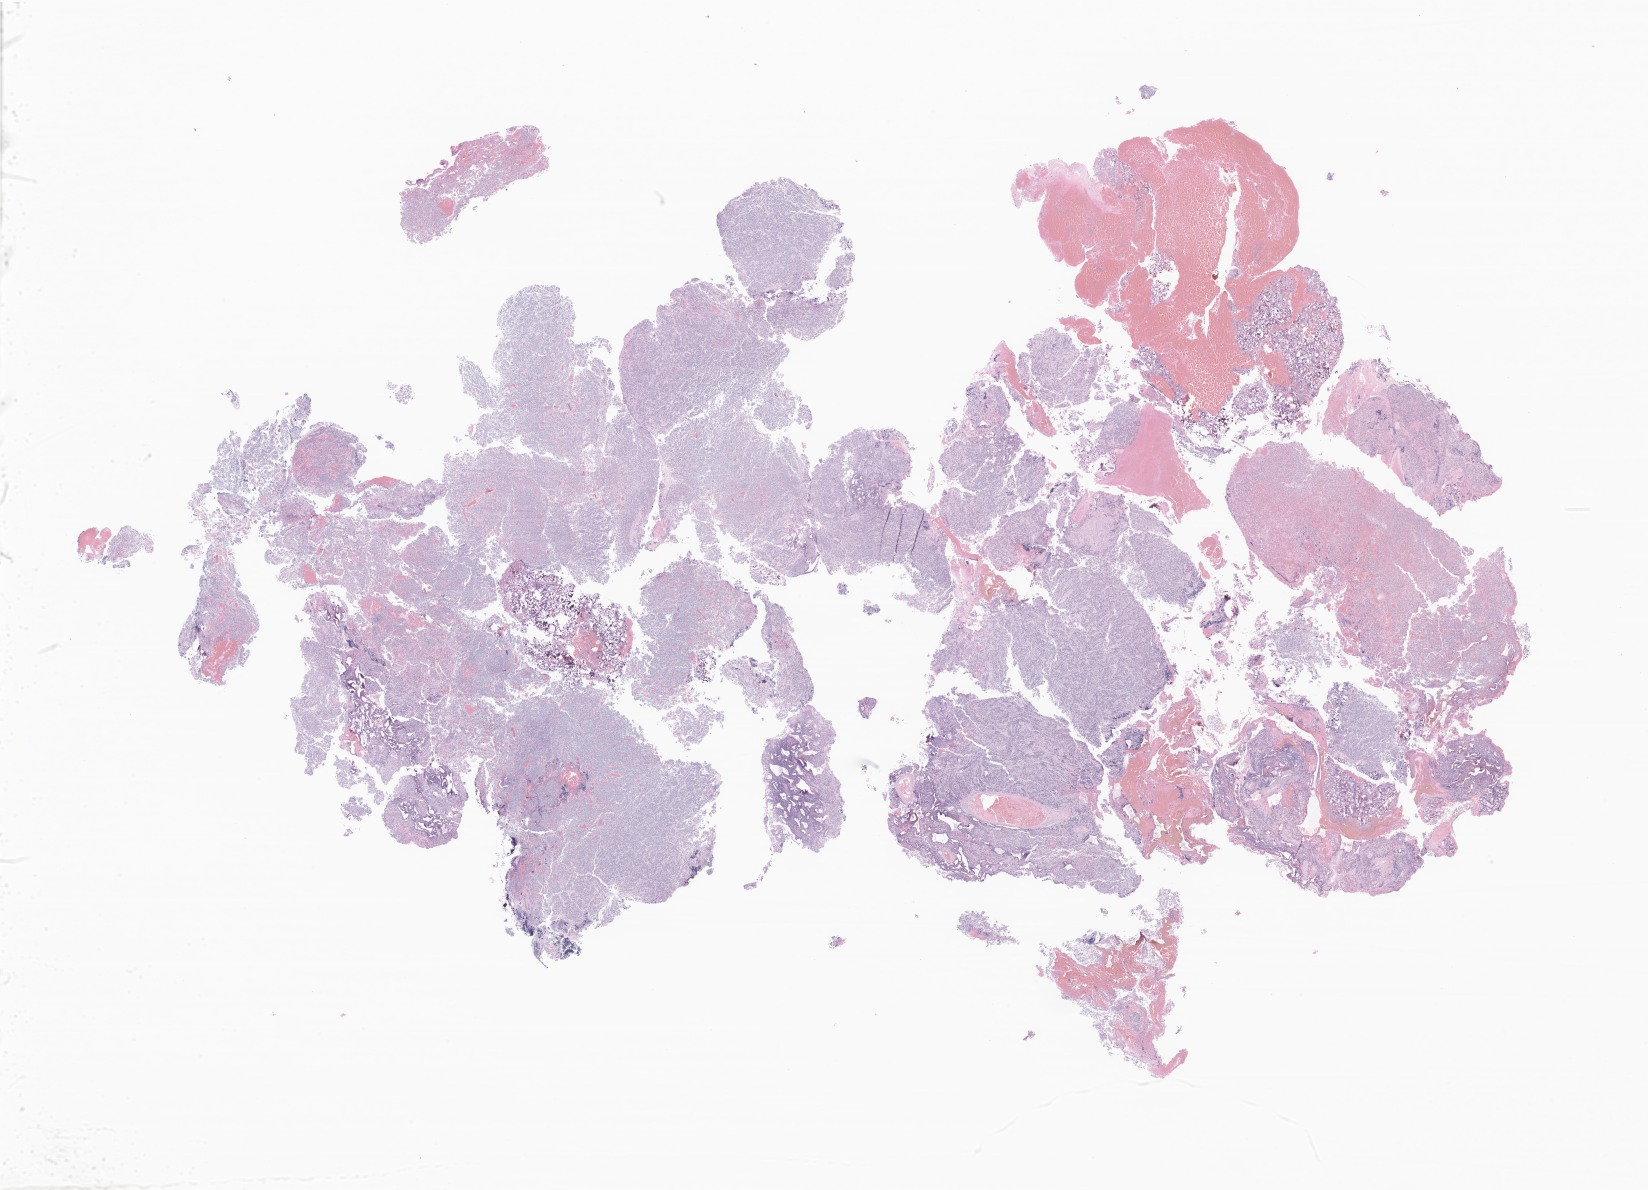
Digitized haematoxylin and eosin-stained section of tumor tissue from the central nervous system, low-resolution overview of the scanned area, about 27.8 x 20.1 mm, formalin-fixed, paraffin-embedded (FFPE) tissue. Female patient, age 206 months.
Recorded diagnosis: Medulloblastoma, NOS.